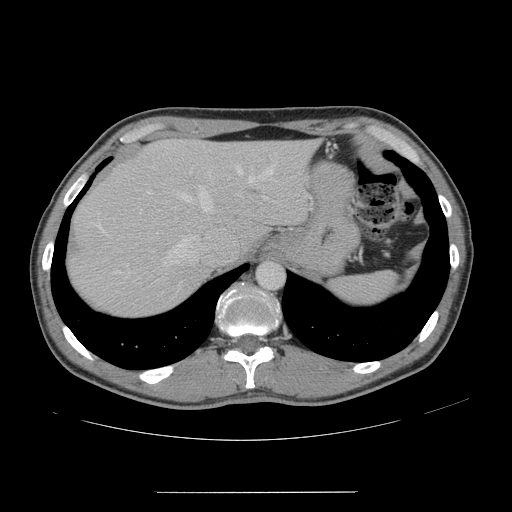
Contrast-enhanced abdominal CT, one axial slice; slice 121 of 178 in the series (ordered by position); 120 kVp; intravenous contrast given; soft-tissue window (W 400 / L 40 HU); 512 × 512 image matrix, field of view 401 × 401 mm. Male patient, age 53 years. Case-level facts recorded for this patient, not image findings: diagnosis: colorectal cancer liver metastases, imaged before liver resection; multiple liver metastases: yes; largest metastasis: 2.4 cm; disease in both lobes: no.
Annotated regions visible in this slice (expert manual segmentation):
- hepatic veins: bounding box [x1, y1, x2, y2] px = [96, 165, 275, 266]
- liver: [68, 140, 317, 317]
- planned liver remnant (the part of the liver to remain after resection): [150, 140, 316, 246]
- portal vein (with intrahepatic branches): [139, 210, 142, 214]